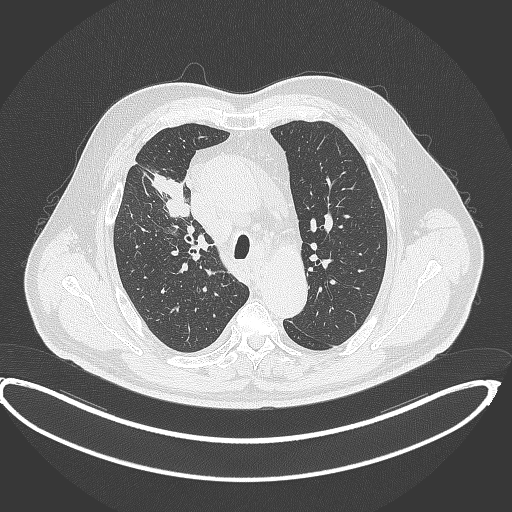
Chest CT, one axial slice. Position 289 of 390 along the scan axis. Reconstruction kernel B70f. 120 kVp. Lung window (W 1500 / L -600 HU). 1 mm slice thickness. 512 × 512 image matrix, field of view 448 × 448 mm. Patient: male, 62 years. From the clinical record (not read from this slice): clinical TNM (as recorded): T1c N3 M1c.
Outlined on this slice (bounding box drawn by a radiologist):
- lung tumour (recorded histology: adenocarcinoma): bounding box (x1, y1, x2, y2) in pixels: (149, 169, 191, 220)